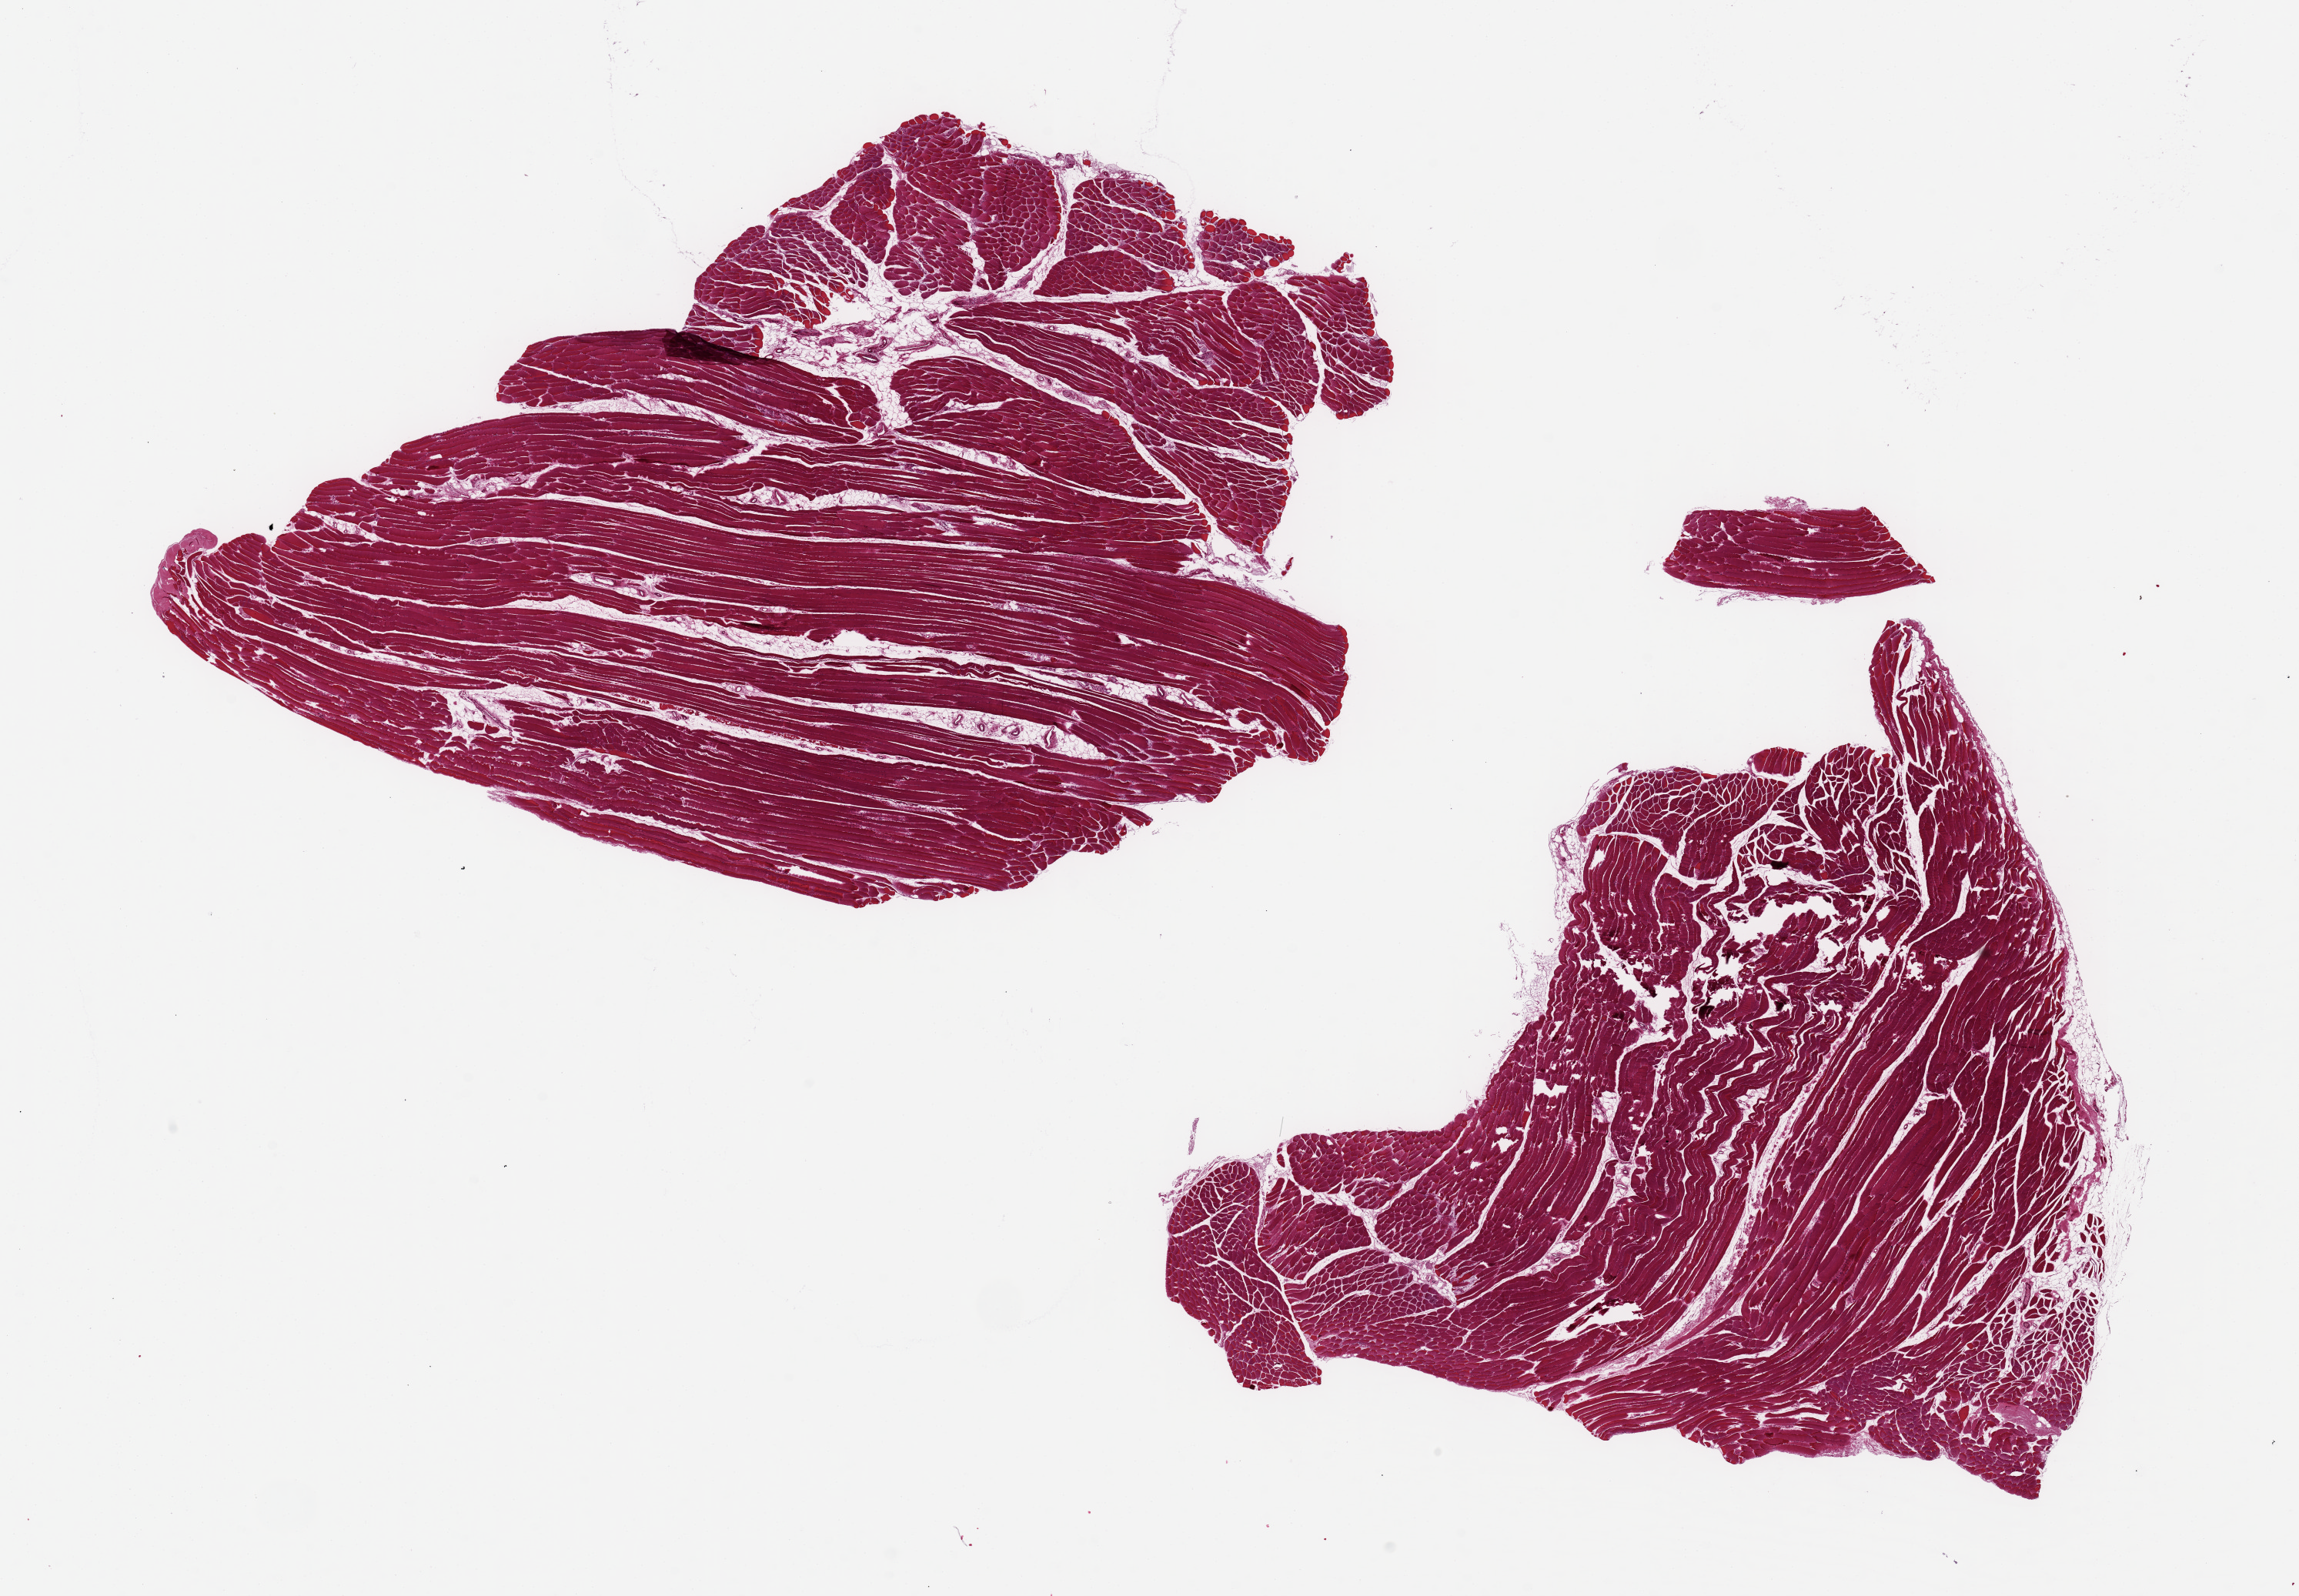
Whole-slide image, H&E stain, low-resolution overview of the scanned area, about 23.6 x 16.4 mm (slide scanned at 20x), PAXgene-fixed paraffin-embedded (PFPE) section, sampled site (target tissue): skeletal muscle, donor tissue sample. Male donor.
Reviewer comment on this tissue sample: 2 pieces 10x7 & 9x9 mm; no adipose.